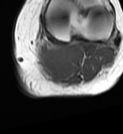
MRI of an extremity soft-tissue mass, one axial slice; slice 48 of 68 in the series (ordered by position); MR volume resampled by the dataset authors to the PET/CT grid (not the native acquisition matrix); 3.27 mm slice thickness; 123 × 134 image matrix, field of view 120 × 131 mm. Female patient. Case-level facts recorded for this patient, not image findings: histological type: extraskeletal high grade osteogenic sarcoma; grade: high; site of the primary tumour: left calf.
Structures marked on this image (expert contour drawn on MRI and transferred to this co-registered scan by the dataset authors):
- gross tumour volume (mass): bounding box <38,46,77,74> (left, top, right, bottom; pixels)